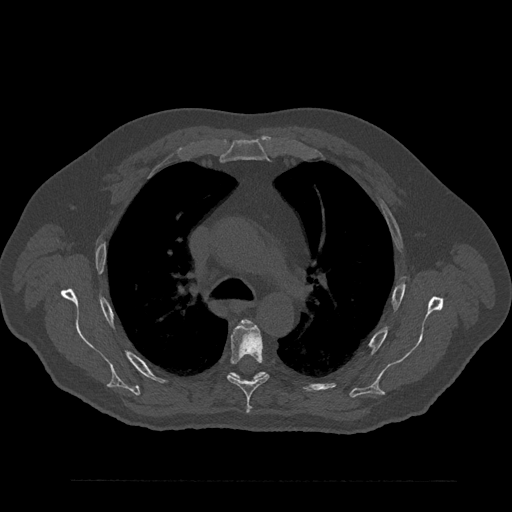
CT including the spine, one axial slice. Position 597 of 797 along the scan axis. Reconstruction kernel Br40s/3. 120 kVp. Bone window (W 1800 / L 400 HU). 0.5 mm slice thickness. 512 × 512 image matrix, field of view 430 × 430 mm. Male patient, age 61 years. Case-level facts recorded for this patient, not image findings: primary cancer: prostate.
Structures marked on this image (semi-automatic segmentation, software-assisted and operator-edited):
- T4 vertebra: bounding box (x1, y1, x2, y2) in pixels: (242, 320, 246, 323)
- T5 vertebra: (227, 324, 269, 409)
- T6 vertebra: (228, 372, 268, 383)